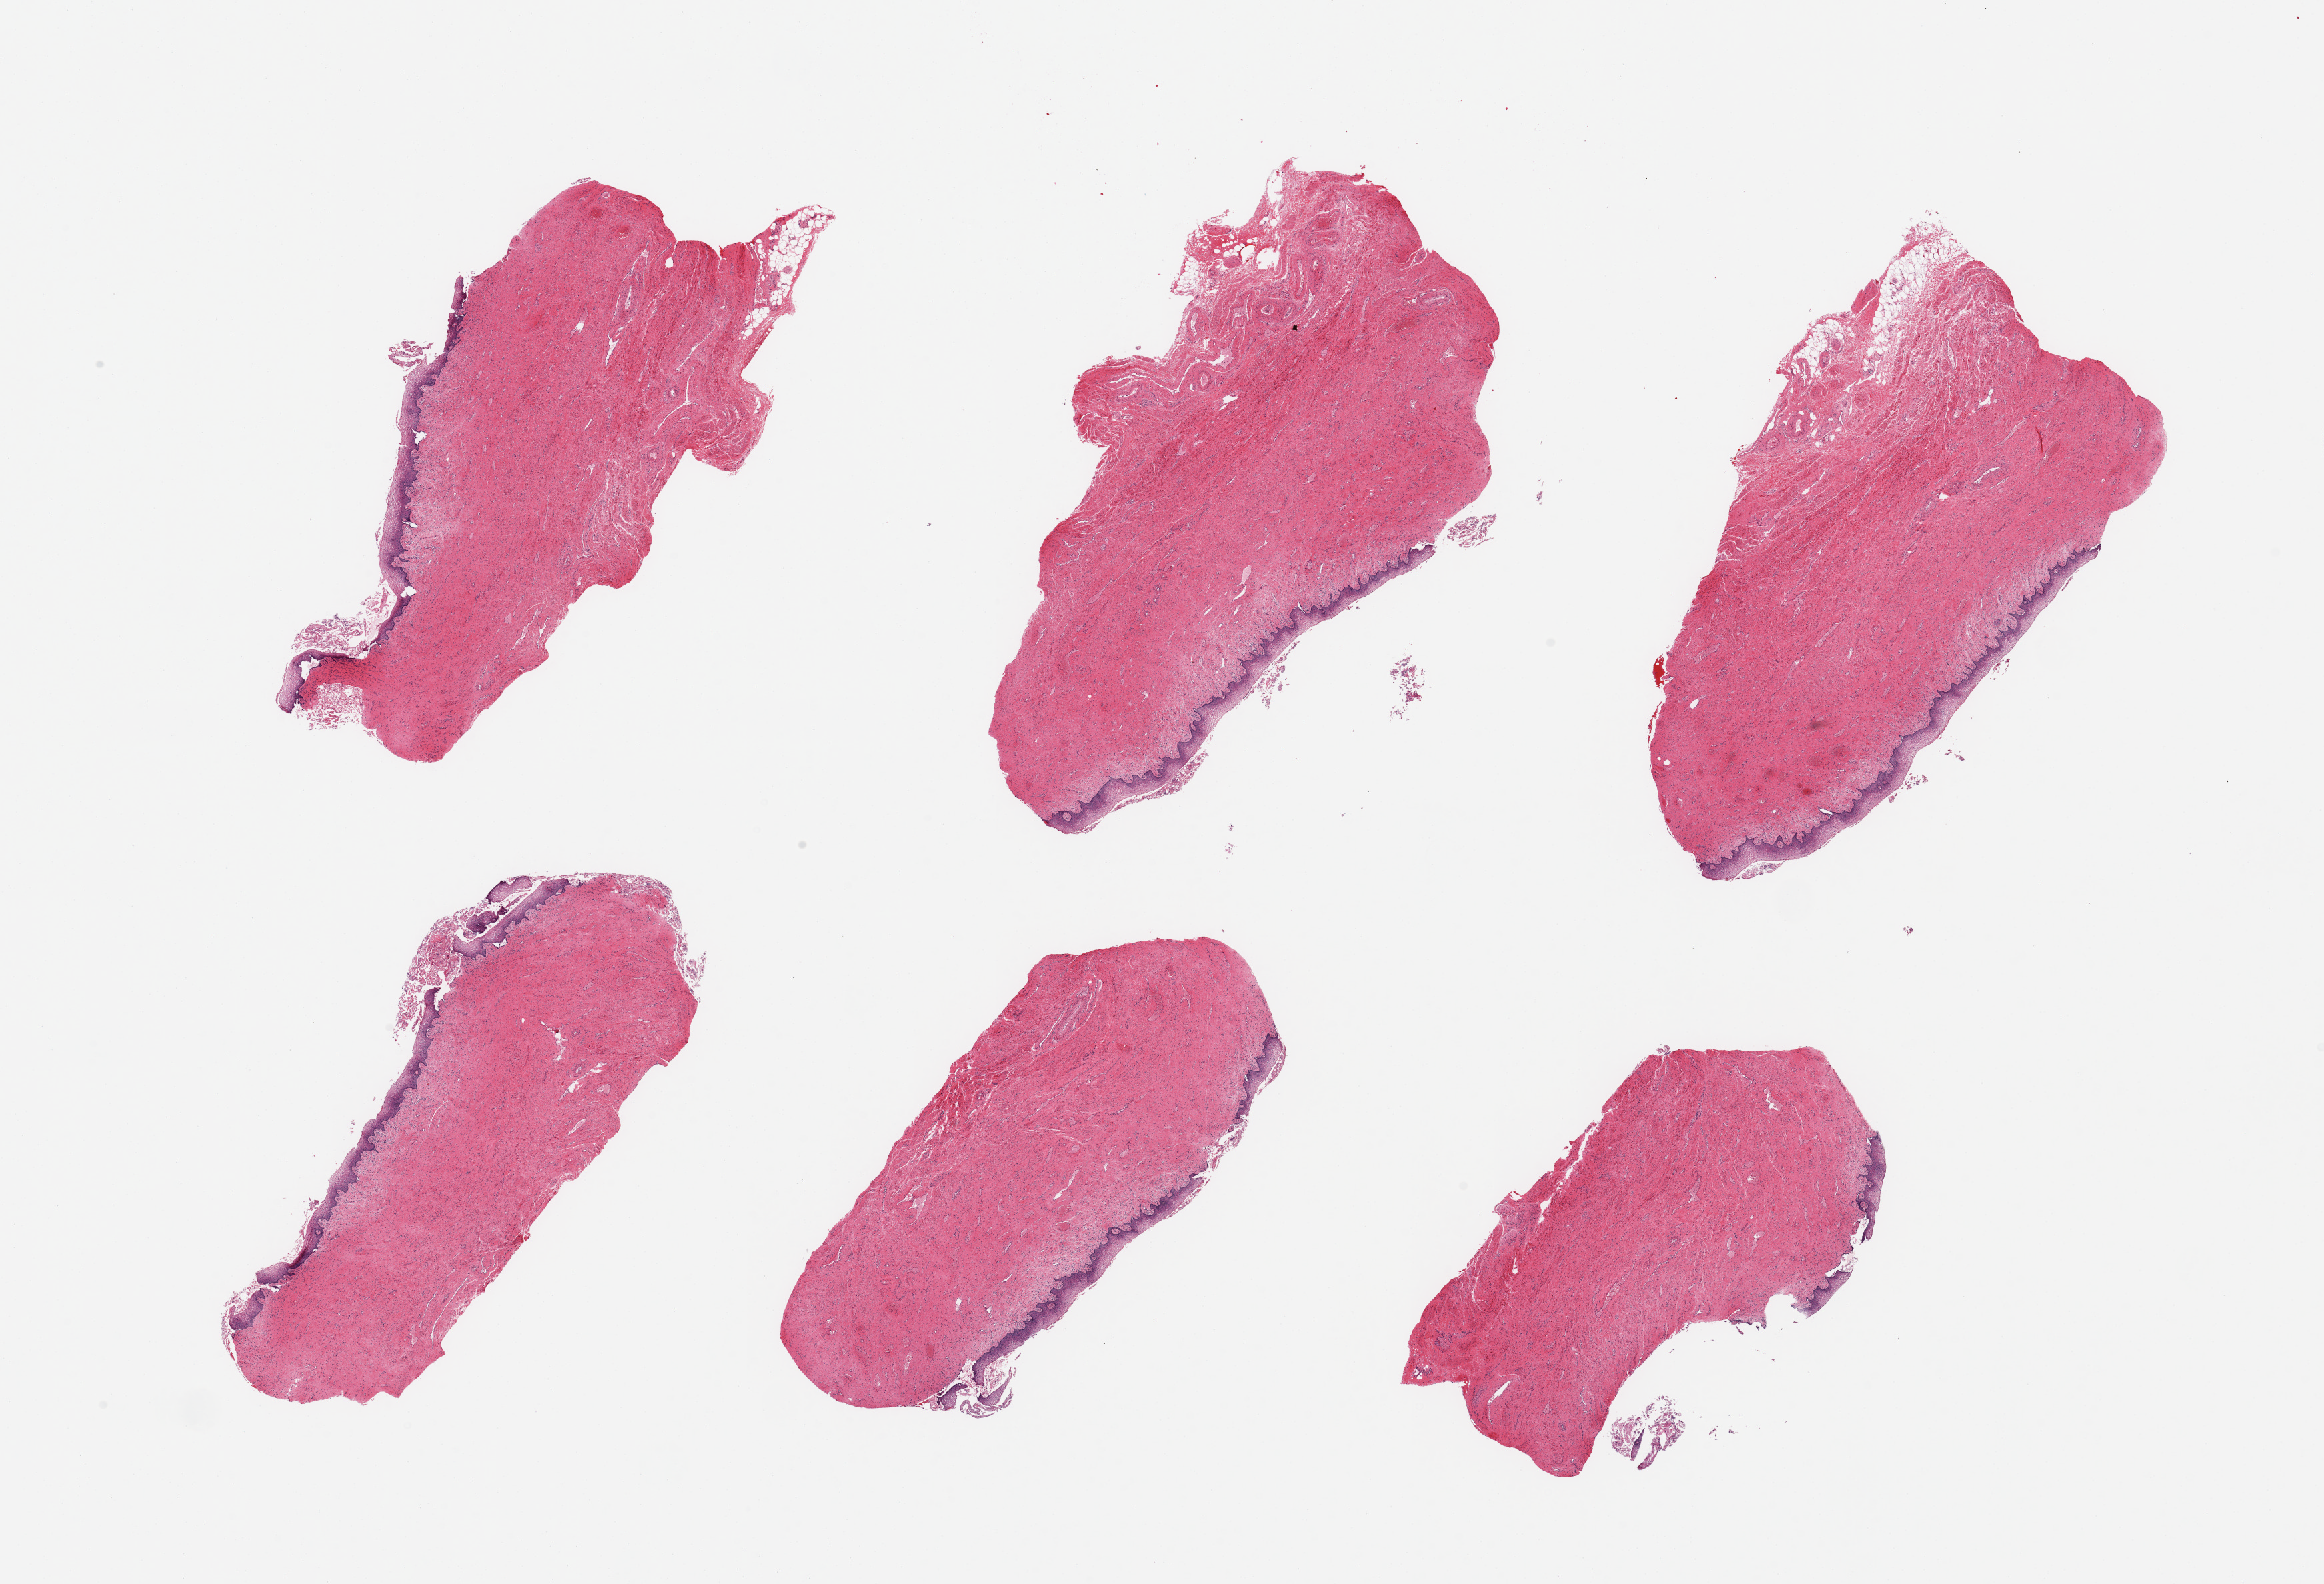
Whole-slide image, H&E stain, a low-resolution overview of the entire scanned area, about 27.6 x 18.8 mm (slide scanned at 20x); PAXgene-fixed paraffin-embedded (PFPE) section; section of vagina (target tissue); donor tissue sample.
* pathologist's review note for this sample: 6 pieces, squamous mucosa is ~0.1-0.2mm